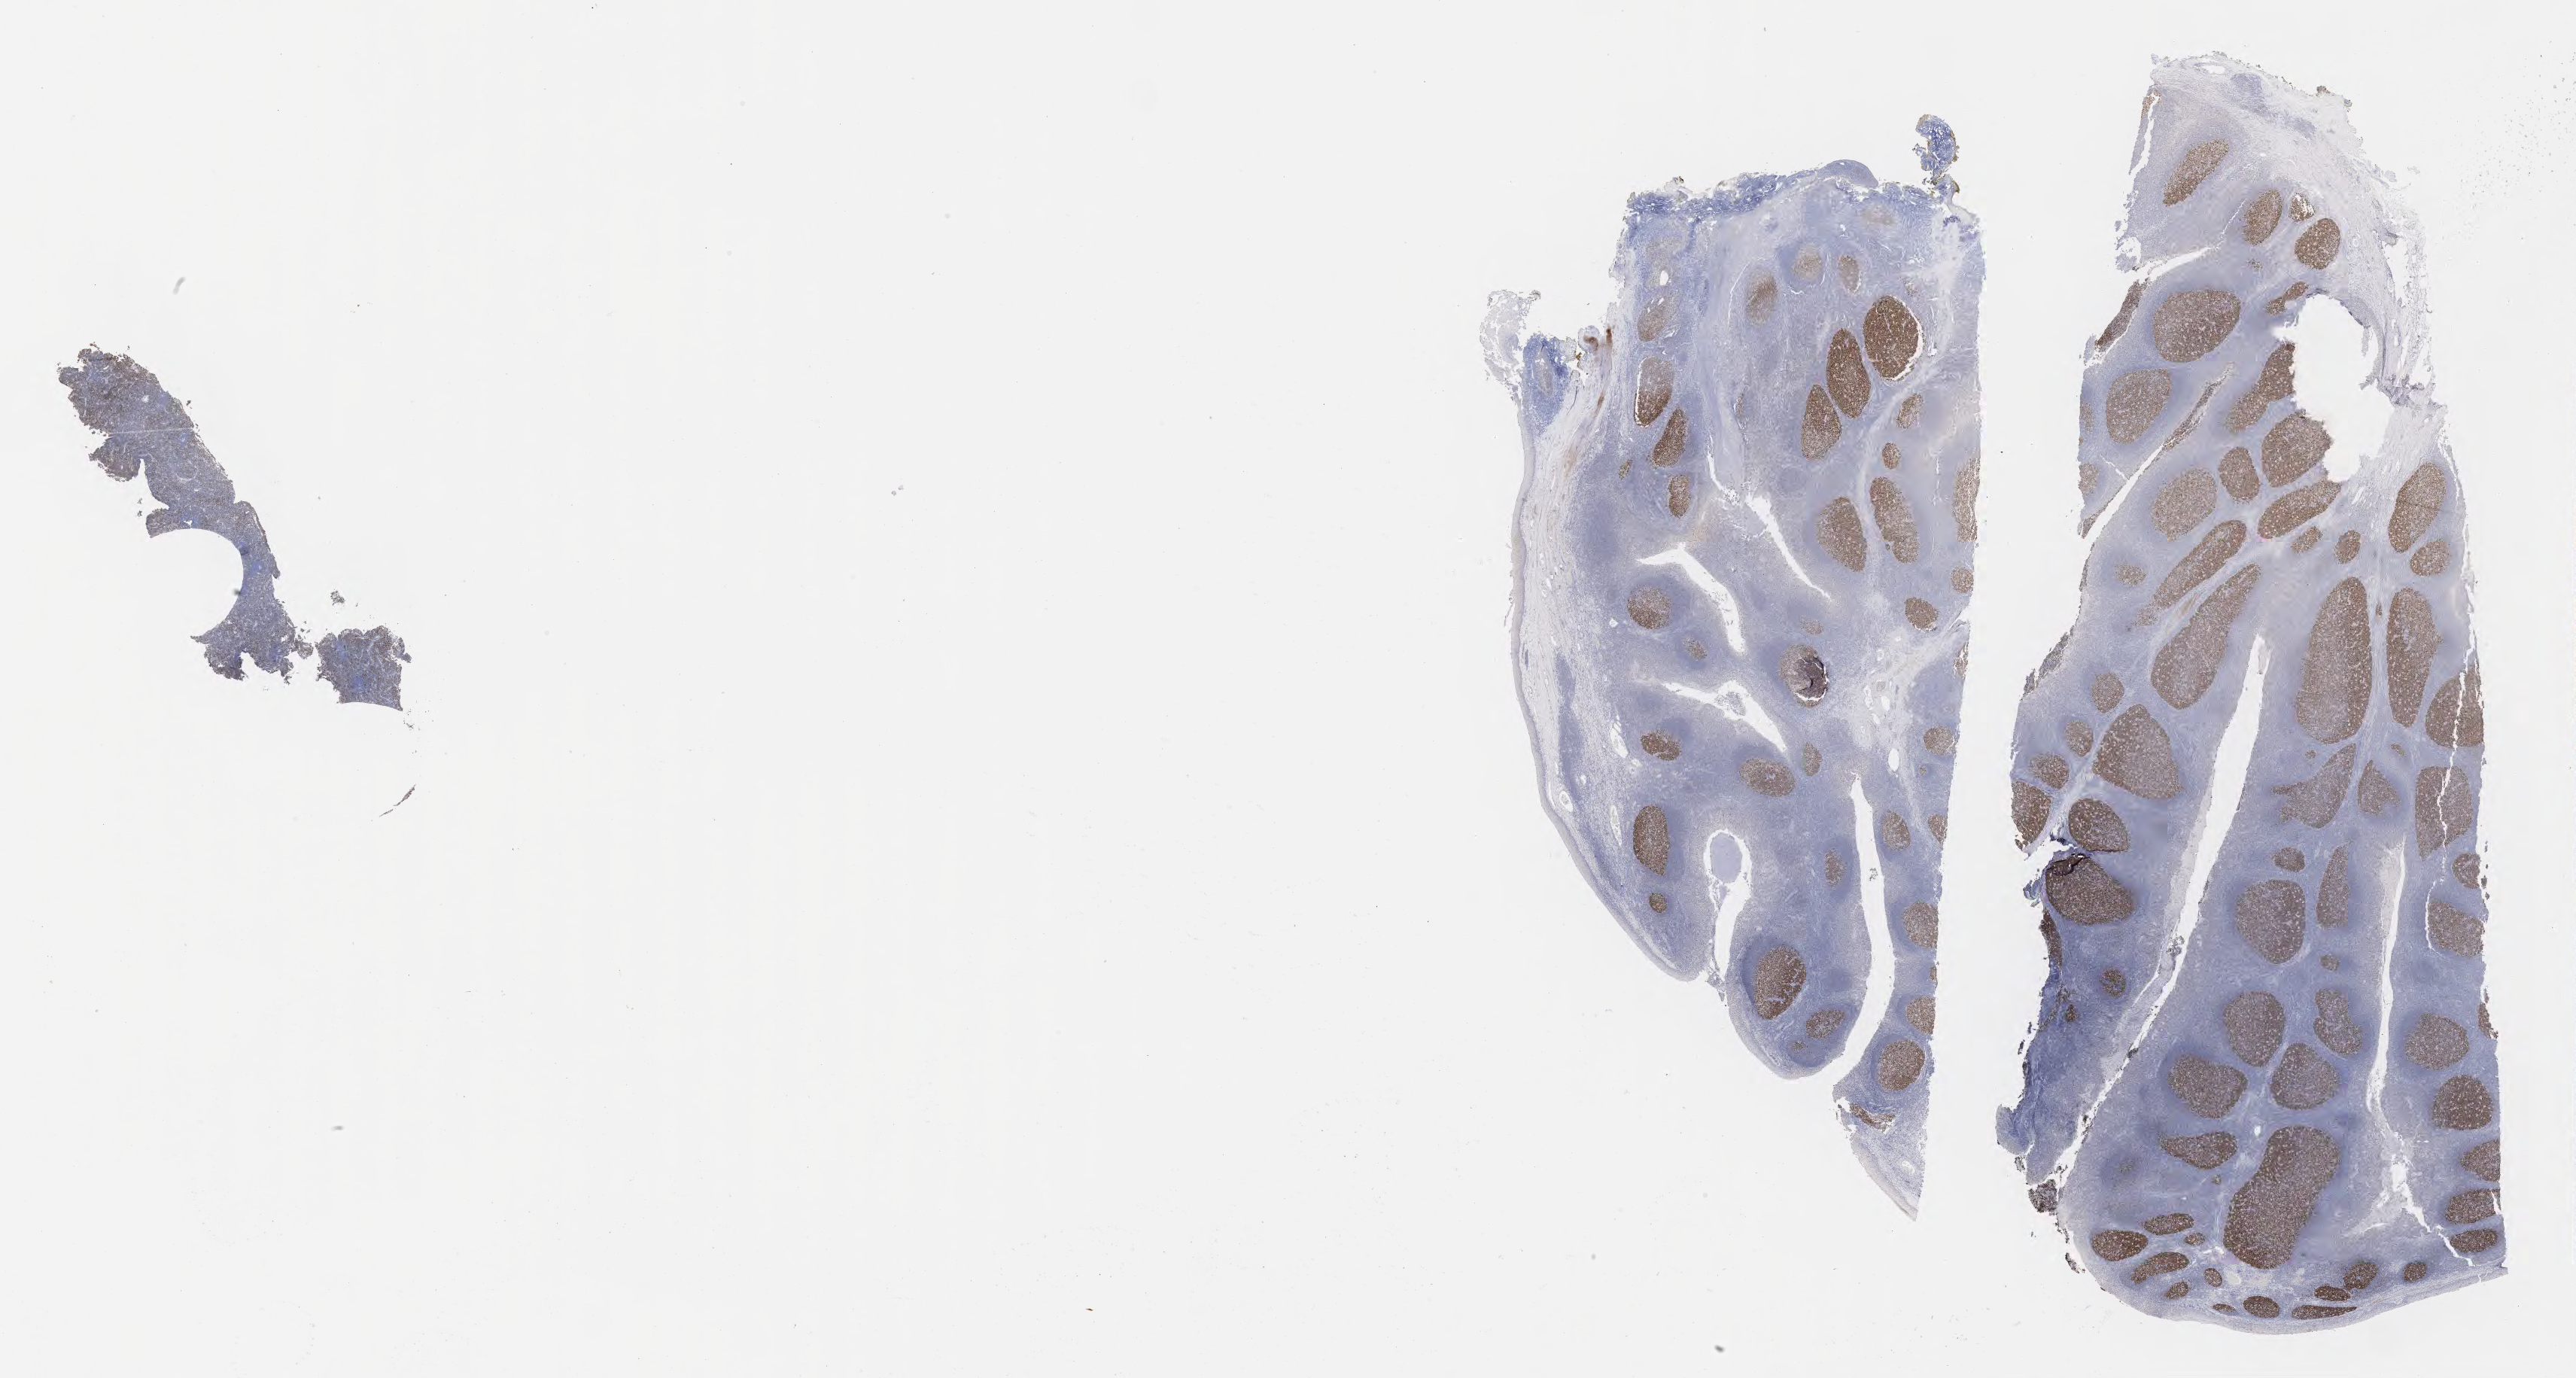
IHC for BCL6, whole-slide image — a low-resolution overview of the entire scanned area, about 27.7 x 14.8 mm, tumor tissue. Male, age 5 years at initial diagnosis.
• diagnosis: Burkitt lymphoma, NOS